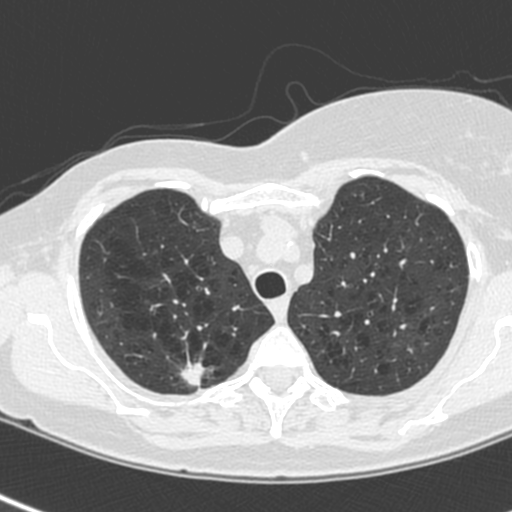
Axial slice from a low-dose chest CT screening exam; baseline annual screen; lung window (W 1500 / L -600 HU); 512 × 512 image matrix, field of view 281 × 281 mm. Female, age 64 years at enrolment. Current smoker at enrolment.
Lesion marked by an expert reader, bounding box (x1, y1, x2, y2) in pixels: (167, 353, 222, 403). Screening reader's record for this exam (one nodule recorded; not confirmed to be the boxed lesion): non-calcified nodule or mass ≥4 mm, right upper lobe, 13 × 10 mm, spiculated (stellate) margins, soft tissue attenuation. Official screen result: positive, change unspecified: nodule(s) >= 4 mm or enlarging nodule(s), mass(es), or other non-specific abnormalities suspicious for lung cancer. Participant outcome: lung cancer diagnosed 21 days after this screen — adenocarcinoma, NOS, right upper lobe, poorly differentiated (G3), stage IIIB (AJCC 6th edition), 20 mm at pathology.